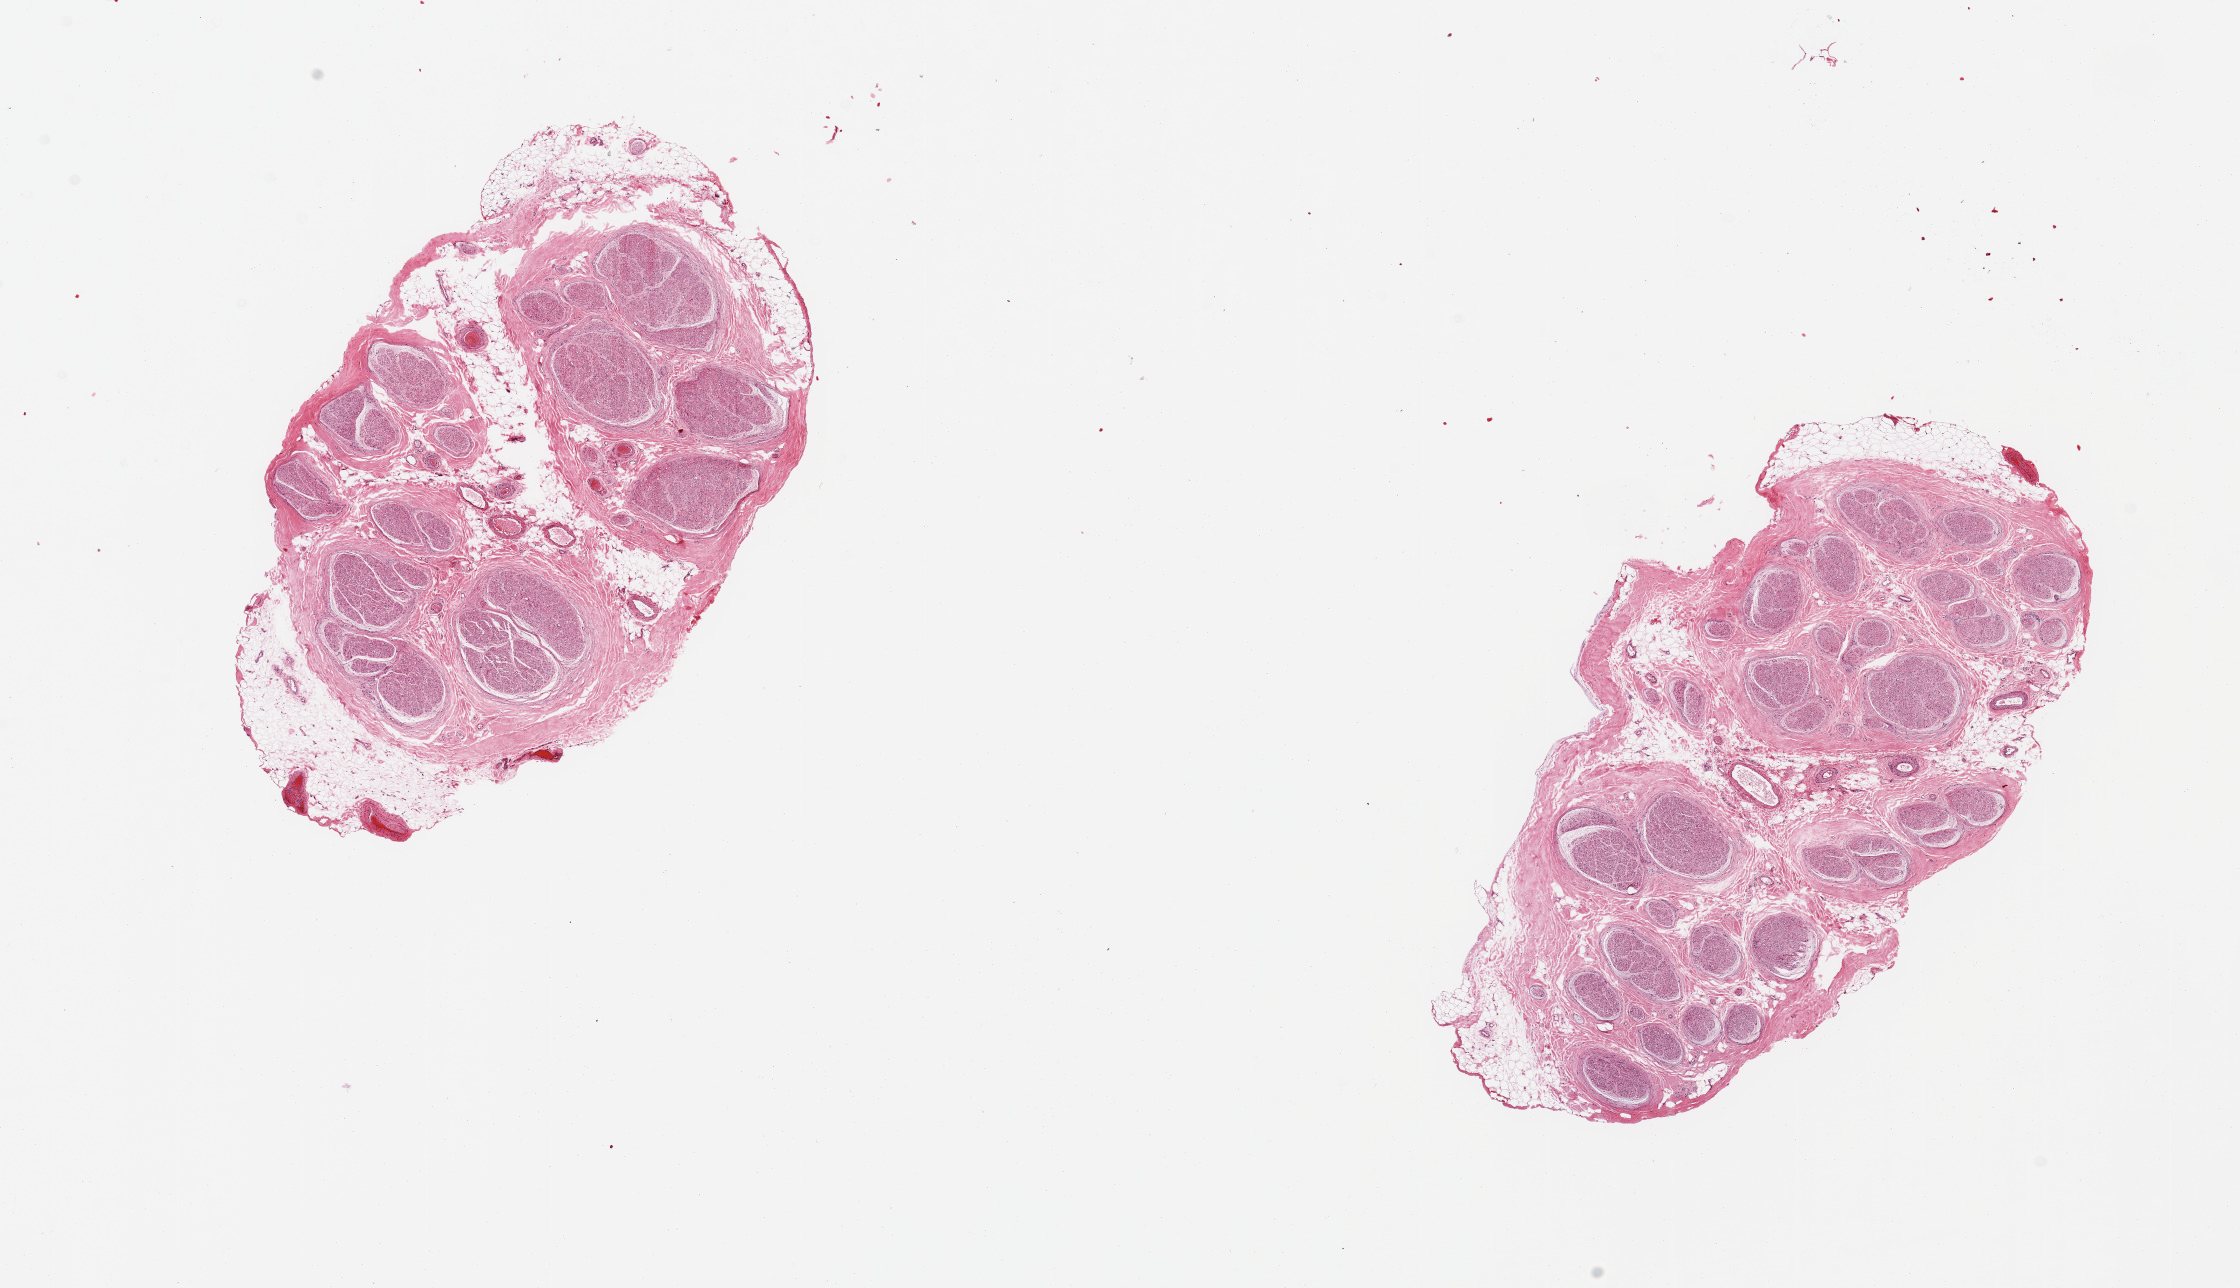
Hematoxylin and eosin (H&E) whole-slide image, low-resolution overview of the scanned area, about 17.7 x 10.2 mm (slide scanned at 20x); PAXgene-fixed, paraffin-embedded tissue; target tissue: tibial nerve; donor tissue sample. Donor: male.
* pathologist's review note for this sample: 2 pieces; includes up to 15-20% internal/external fat